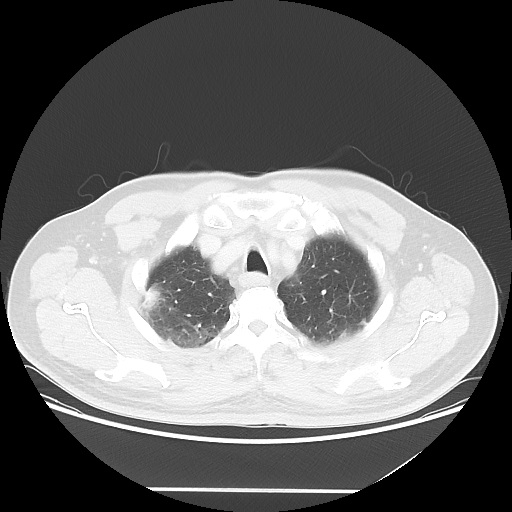
Chest CT, one axial slice. Slice 45 of 54 in the series (ordered by position). Reconstruction kernel LUNG. Lung window (W 1500 / L -600 HU). 5 mm slice thickness. 512 × 512 image matrix, field of view 416 × 416 mm. Male patient, age 65 years. From the clinical record (not read from this slice): clinical TNM (as recorded): T1c N1 M0.
Annotated regions visible in this slice (rectangle marked by the reading radiologist):
- lung tumour (recorded histology: adenocarcinoma): bounding box (x1, y1, x2, y2) in pixels: (141, 282, 166, 321)